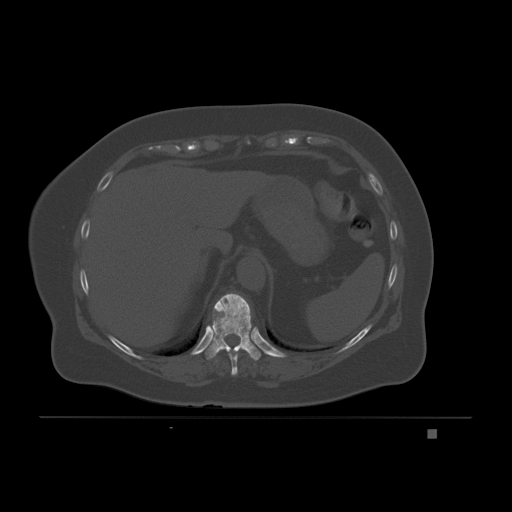
CT including the spine, one axial slice; slice 102 of 221 in the series (ordered by position); bone window (W 1800 / L 400 HU); 3 mm slice thickness; 512 × 512 image matrix, field of view 474 × 474 mm. Female patient, age 63 years. Case-level facts recorded for this patient, not image findings: primary cancer: breast.
Outlined on this slice (semi-automatic segmentation, software-assisted and operator-edited):
- T10 vertebra: bounding box [x1, y1, x2, y2] px = [205, 293, 261, 361]
- T9 vertebra: [228, 352, 239, 376]